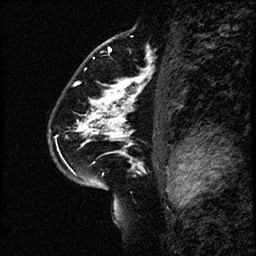
Breast MRI (dynamic contrast-enhanced), one sagittal slice. Slice 40 of 60 in the series (ordered by position). Dynamic contrast-enhanced study with each time point stored as its own series, time point 2 of 4 at this slice position (early post-contrast, ordered by acquisition time). 1.5 T. TE 4.2 ms, TR 17.6 ms. 256 × 256 image matrix, field of view 200 × 200 mm. Female patient, age 43 years. From the clinical record (not read from this slice): setting: breast cancer imaged before/during neoadjuvant chemotherapy.
Annotated regions visible in this slice (semi-automatically segmented with operator editing):
- analysis volume of interest (the breast-tissue region the enhancement analysis was run in; not a lesion): bounding box <52,57,169,190> (left, top, right, bottom; pixels)
- tumour enhancement mask (voxels above the 100 % enhancement threshold inside the analysis volume of interest): <81,82,133,142>